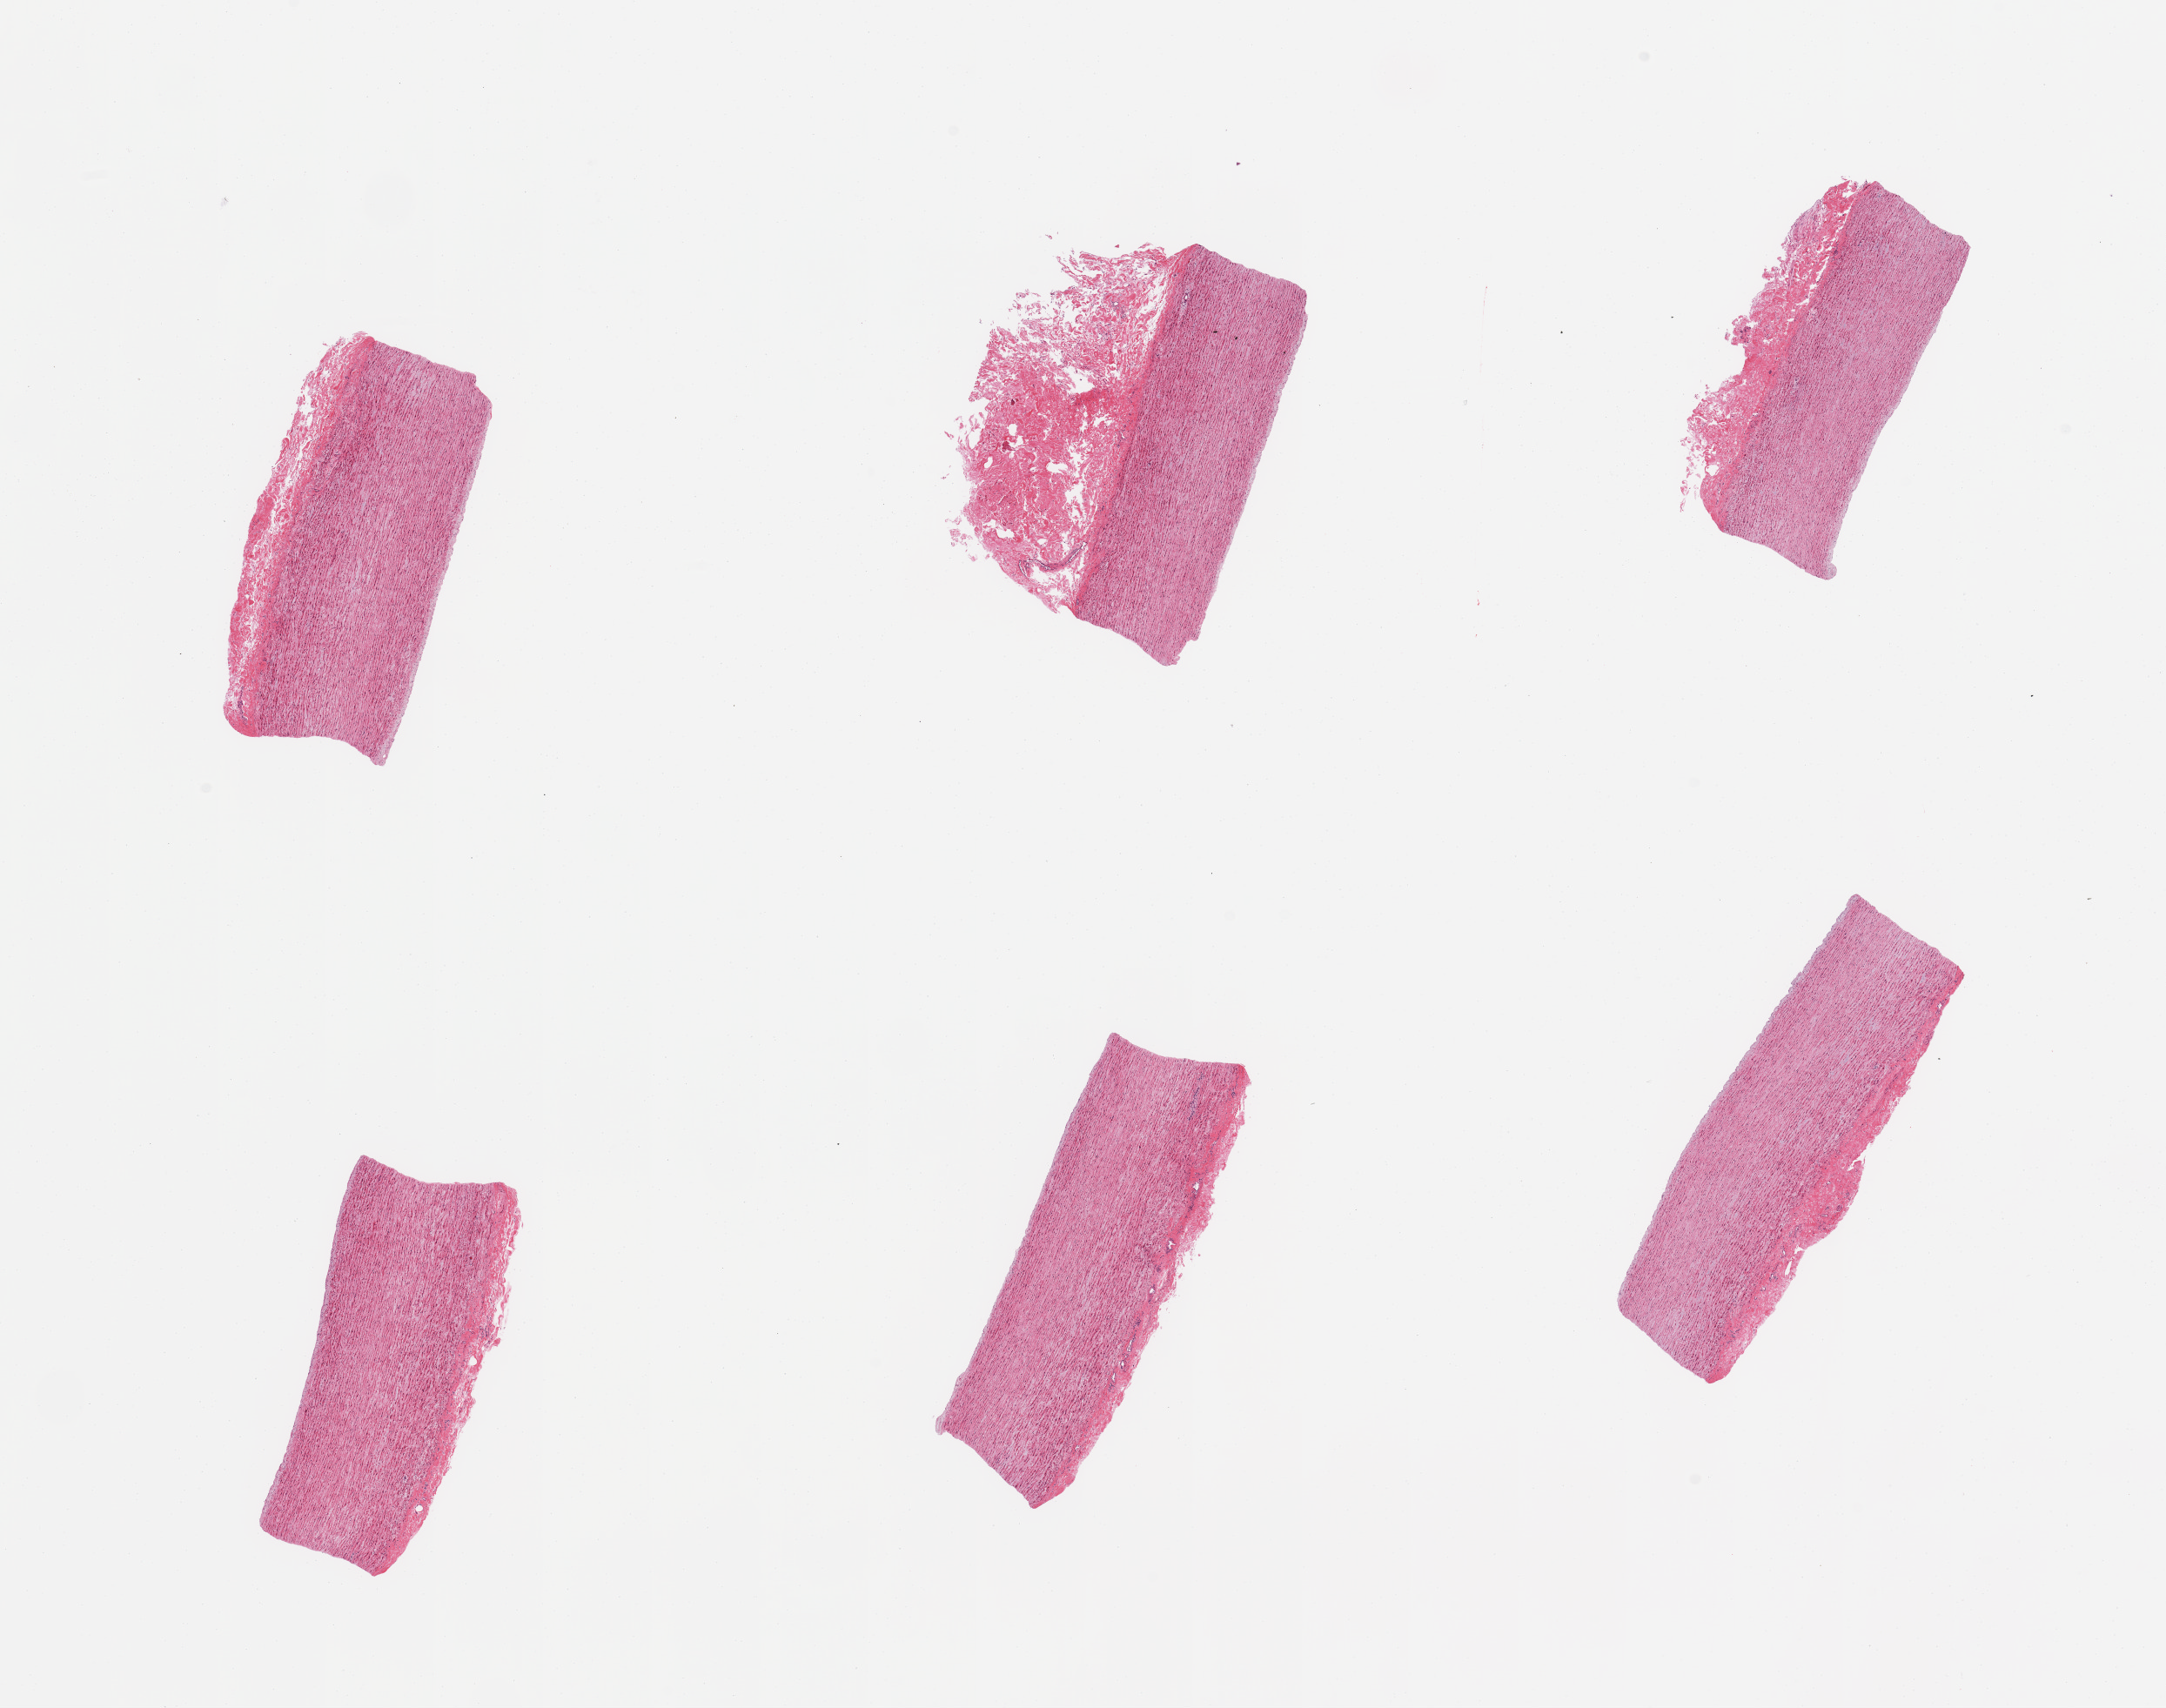
Whole-slide image, hematoxylin and eosin (H&E) stain — low-resolution overview of the scanned area, about 19.7 x 15.5 mm; PAXgene-fixed paraffin-embedded (PFPE) section; section of aorta (target tissue); donor tissue sample. Female donor.
Reviewer comment on this tissue sample: 2 pieces, adherent nubbins of faxica/fat; not significant atherosis.